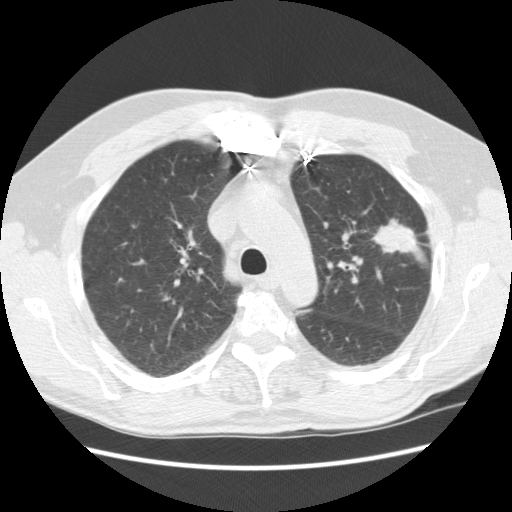
Low-dose screening chest CT, one axial slice. Slice 173 of 231 in the series (ordered by position). Reconstruction kernel STANDARD. Lung window (W 1500 / L -600 HU). 2.5 mm slice thickness. 512 × 512 image matrix, field of view 362 × 362 mm.
Outlined on this slice (expert manual segmentation):
- lesion 1 (tumor, upper lobe of left lung): bounding box (x1, y1, x2, y2) in pixels: (373, 219, 420, 253)